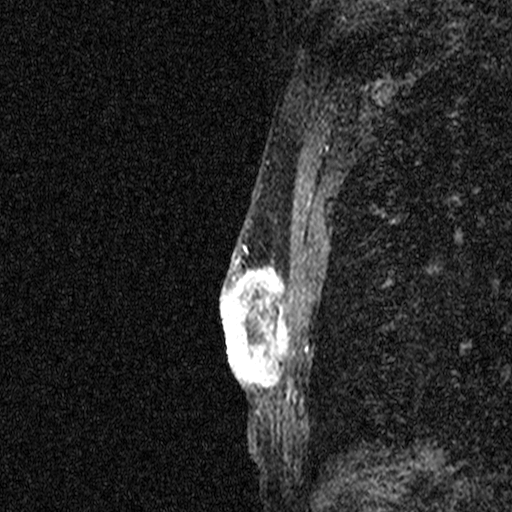
Breast MRI (dynamic contrast-enhanced), one sagittal slice. Position 29 of 44 along the scan axis. Dynamic contrast-enhanced study with each time point stored as its own series, time point 2 of 3 at this slice position (early post-contrast, ordered by acquisition time). 1.5 T. TE 4.5 ms, TR 11 ms. 512 × 512 image matrix, field of view 200 × 200 mm. Patient: female, 44 years. From the clinical record (not read from this slice): setting: breast cancer imaged before/during neoadjuvant chemotherapy; receptor status: HR-positive, HER2-negative.
Structures marked on this image (semi-automatically segmented with operator editing):
- analysis volume of interest (the breast-tissue region the enhancement analysis was run in; not a lesion): box from (x=204, y=254) to (x=294, y=401) px
- tumour enhancement mask (voxels above the 90 % enhancement threshold inside the analysis volume of interest): (x=220, y=254)–(x=288, y=401)